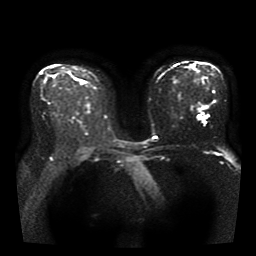
Breast MRI, one axial slice. Position 22 of 41 along the scan axis. Diffusion-weighted series; image 2 of 4 stored at this slice position (different b-values; order by instance number). 1.5 T. 5 mm slice thickness. 256 × 256 image matrix, field of view 330 × 330 mm. Female patient.
Structures marked on this image (outlined manually by an expert reader):
- tumour on diffusion-weighted imaging: bounding box (x1, y1, x2, y2) in pixels: (77, 79, 84, 83)